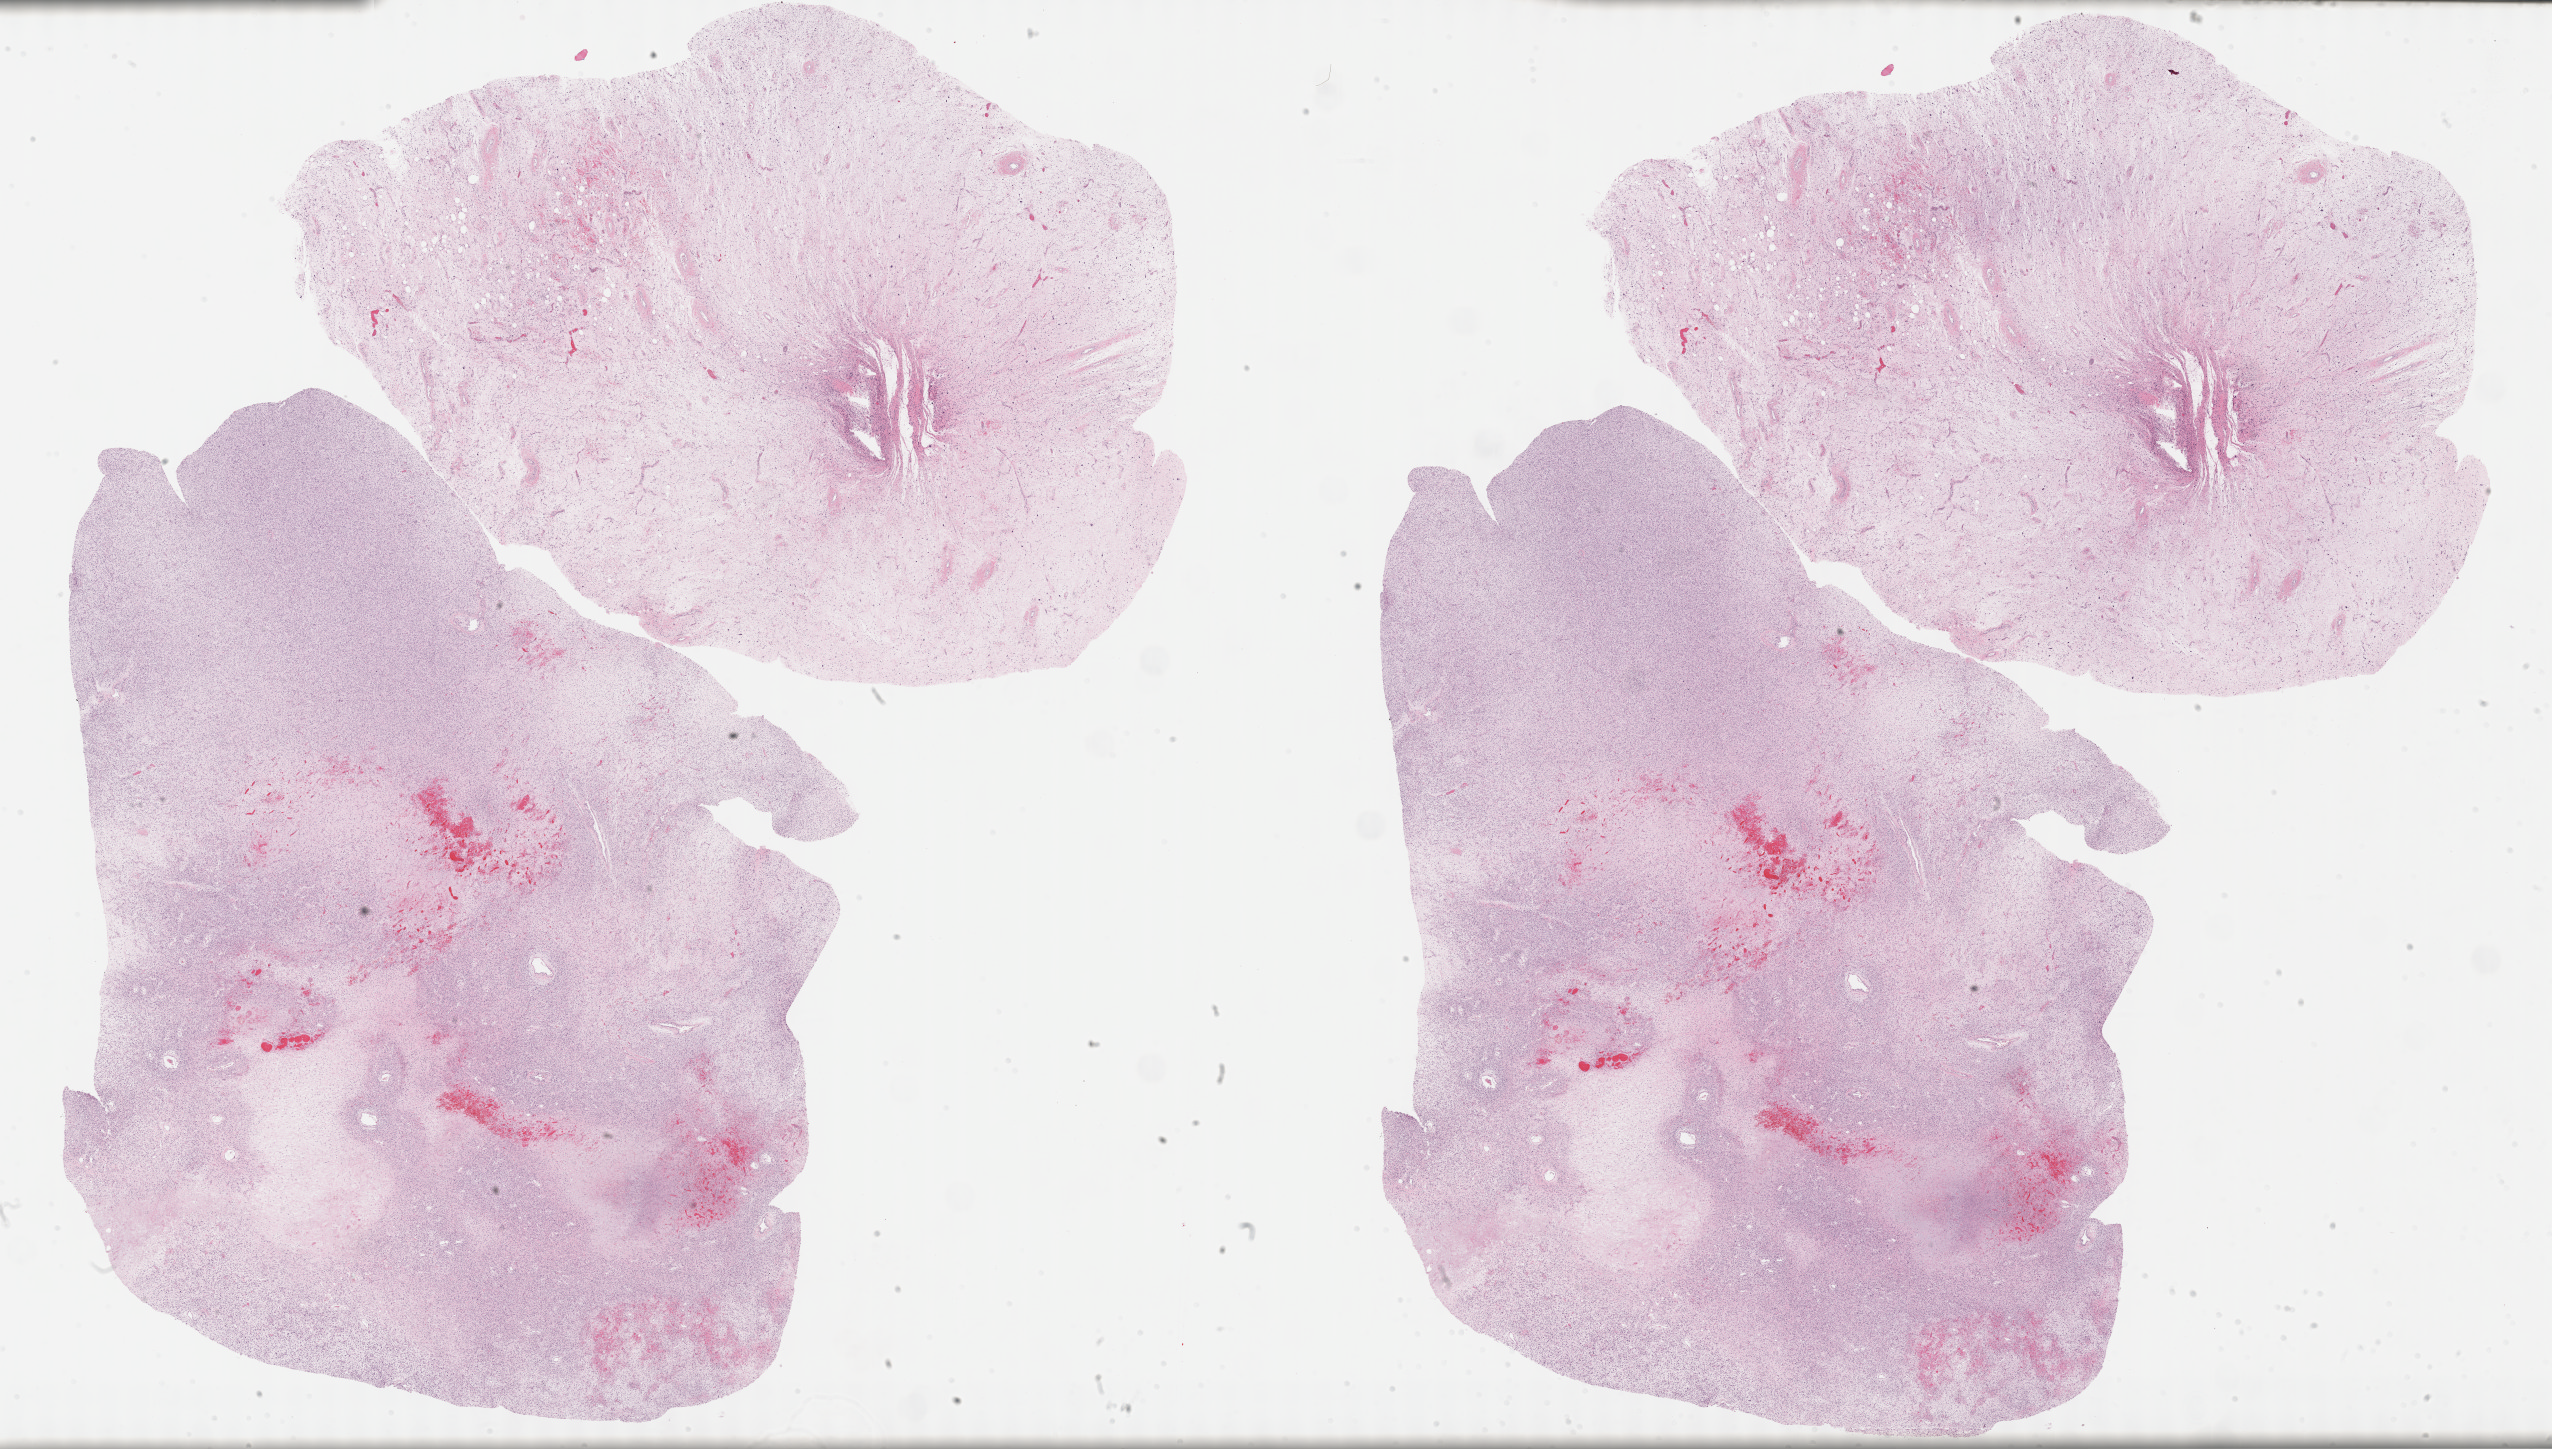
Digitized Hematoxylin and eosin (H&E) stained tissue section (whole slide), a low-resolution overview of the entire scanned area, about 41.3 x 23.4 mm, FFPE section, sample: primary tumour, retroperitoneum and peritoneum. Female, age 76 years at initial diagnosis.
Pathologic diagnosis: Dedifferentiated liposarcoma (retroperitoneum).